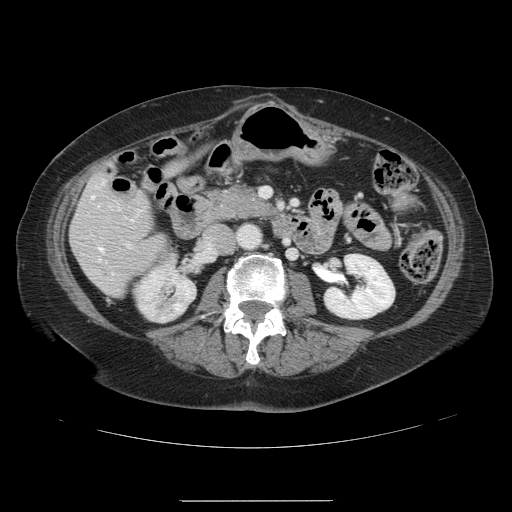
Contrast-enhanced abdominal CT, one axial slice. Position 41 of 141 along the scan axis. Soft-tissue window (W 400 / L 40 HU). 2.5 mm slice thickness. 512 × 512 image matrix. Female patient, age 74 years. From the clinical record (not read from this slice): diagnosis: colorectal cancer liver metastases, imaged before liver resection; multiple liver metastases: yes; largest metastasis: 7 cm; disease in both lobes: yes.
Structures marked on this image (outlined manually by an expert reader):
- hepatic veins: bounding box [x1, y1, x2, y2] px = [91, 180, 104, 251]
- liver: [71, 175, 165, 295]
- planned liver remnant (the part of the liver to remain after resection): [71, 175, 165, 287]
- portal vein (with intrahepatic branches): [126, 244, 130, 246]
- liver metastasis: [137, 272, 141, 274]